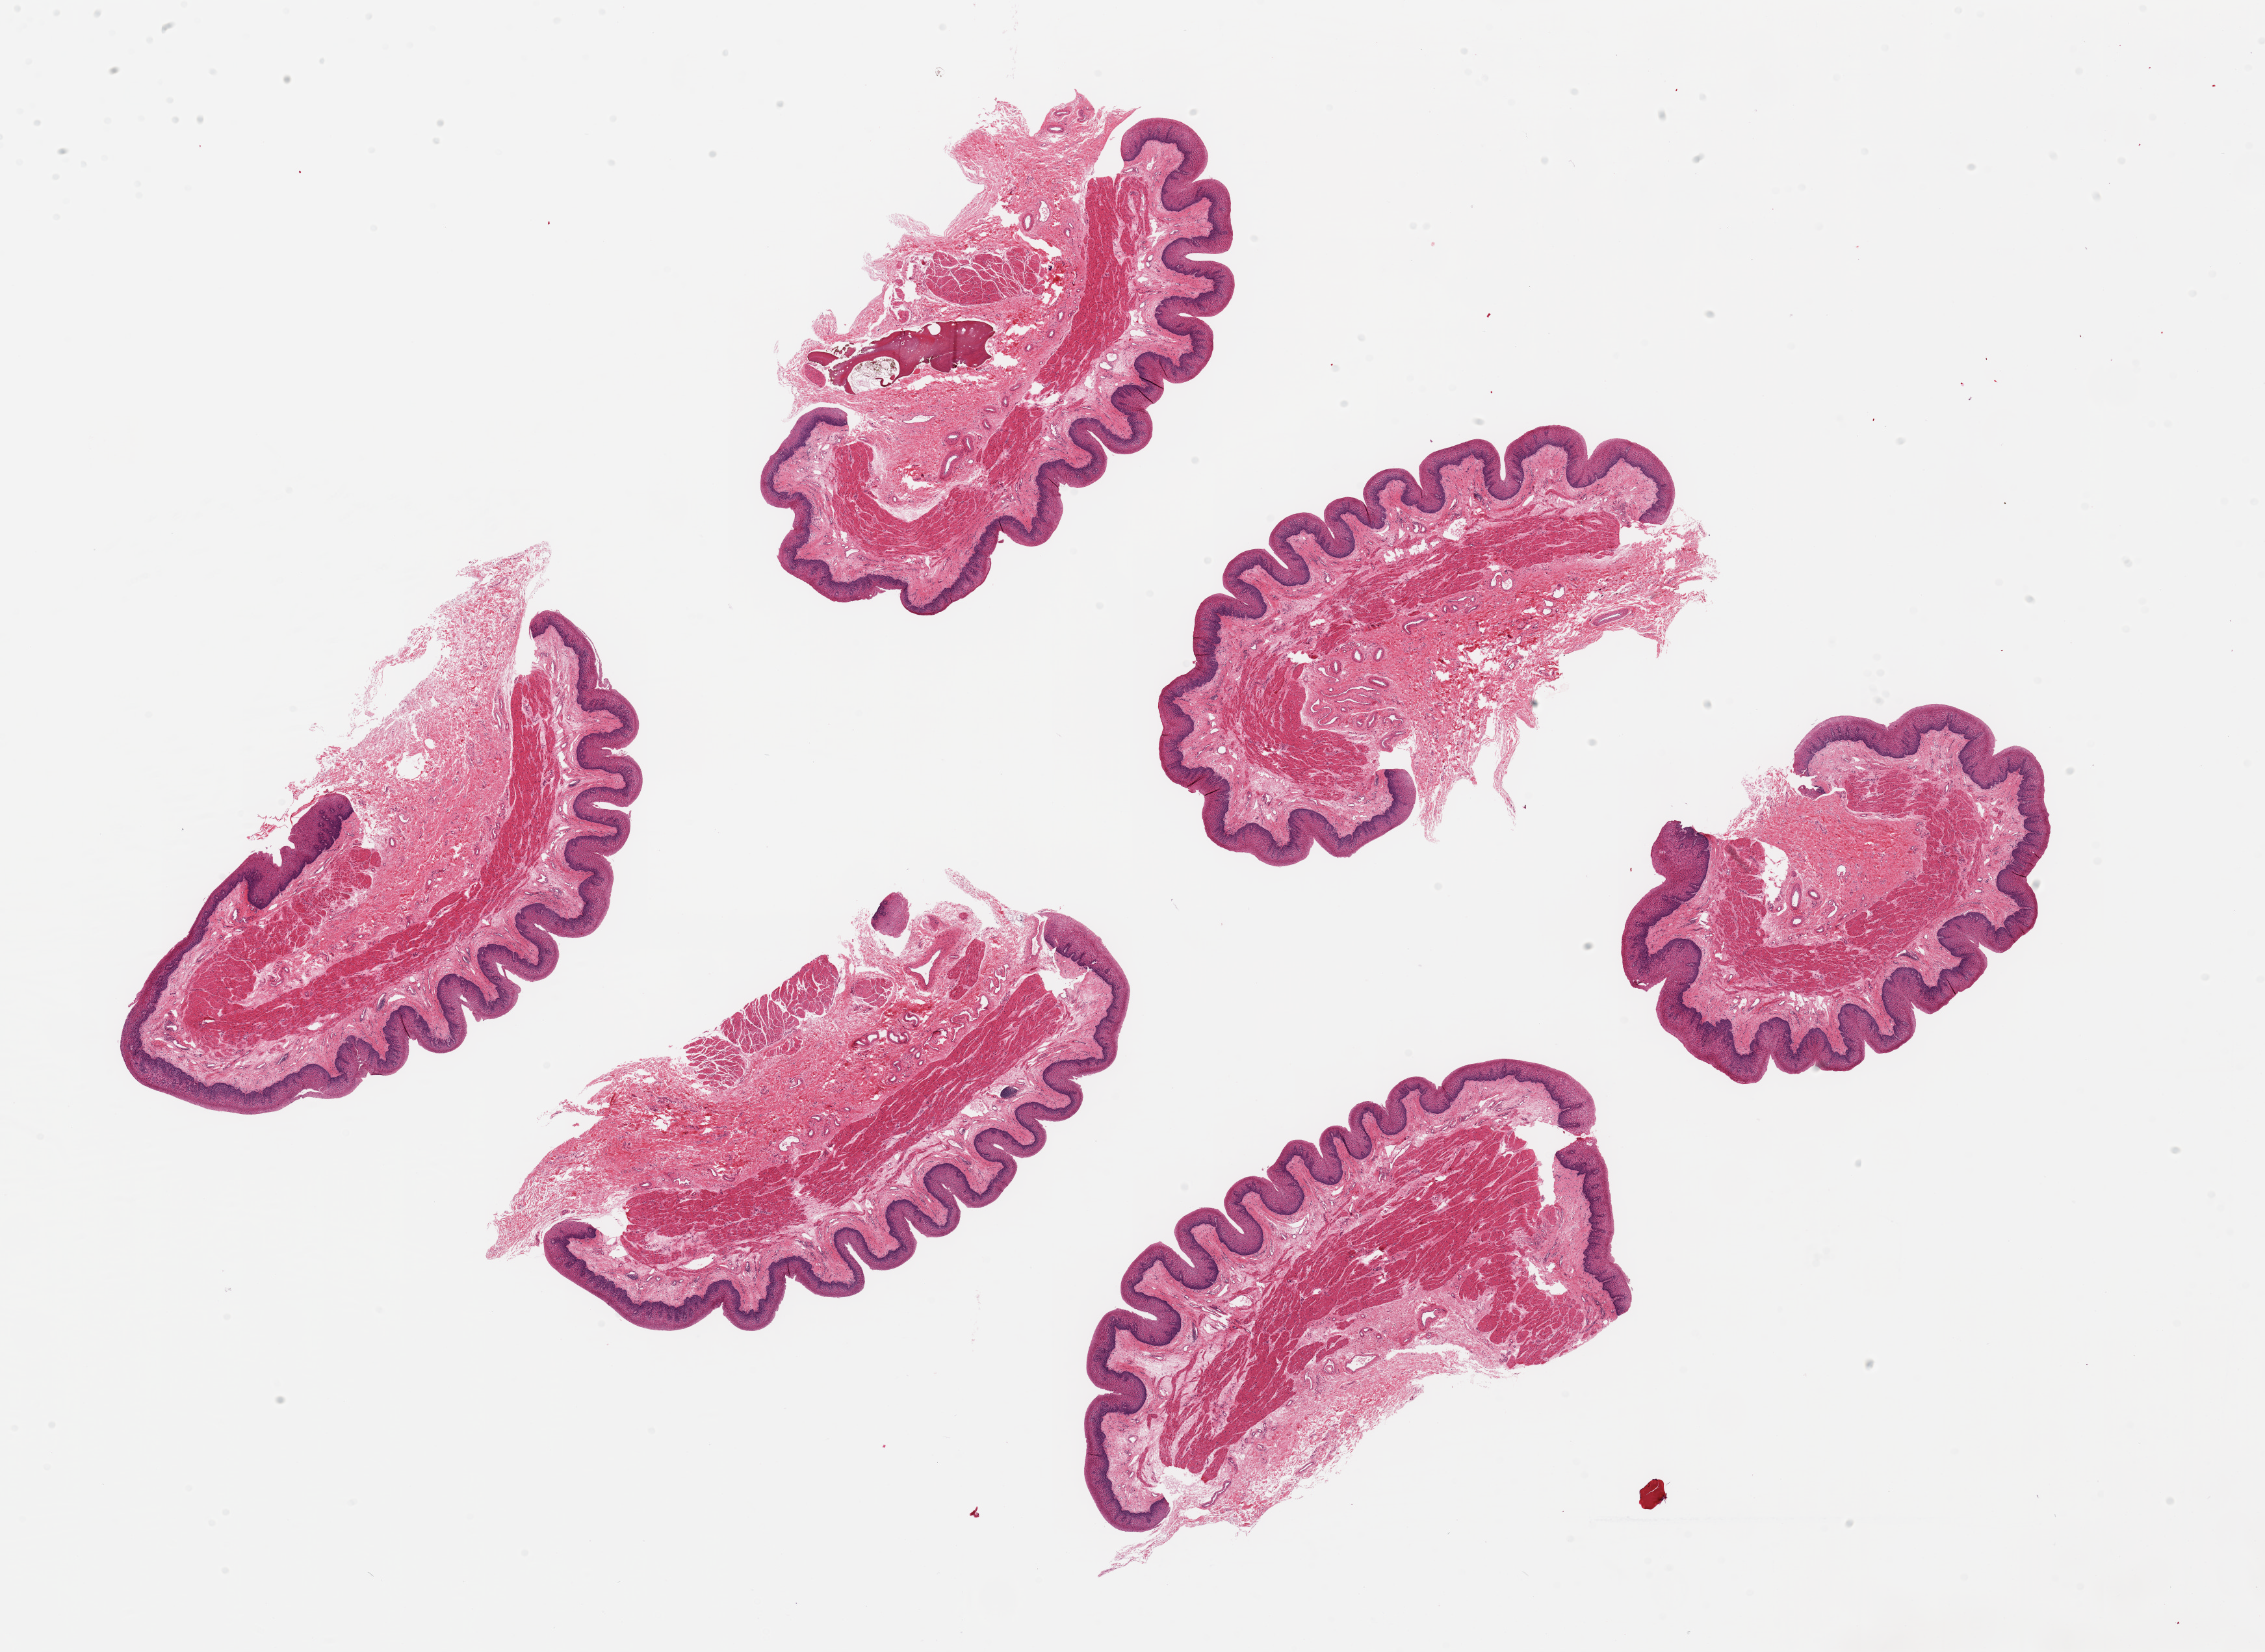
Digitized hematoxylin and eosin (H&E)-stained section — whole scanned area (about 27.6 x 20.1 mm, slide scanned at 20x) shown as a low-resolution overview. PAXgene-fixed, paraffin-embedded tissue. Sampled site (target tissue): esophageal mucous membrane. Tissue donor sample. Donor: male.
- pathologist's review note for this sample: 6 pieces ~7x4mm. Squamous mucosa is ~10% of thickness, well-preserved